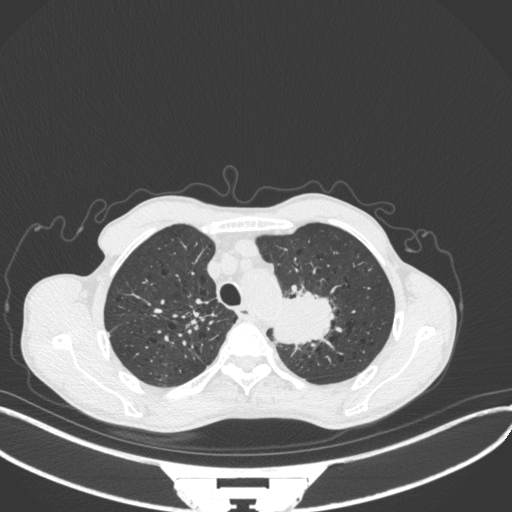
Chest CT, one axial slice; slice 337 of 394 in the series (ordered by position); reconstruction kernel B31f; 120 kVp; lung window (W 1500 / L -600 HU); 512 × 512 image matrix. Patient: male, 65 years. Case-level facts recorded for this patient, not image findings: clinical TNM (as recorded): T2b N0 M0; histopathological grade: G2.
Structures marked on this image (rectangle marked by the reading radiologist):
- lung tumour (recorded histology: adenocarcinoma): bounding box <267,281,333,346> (left, top, right, bottom; pixels)